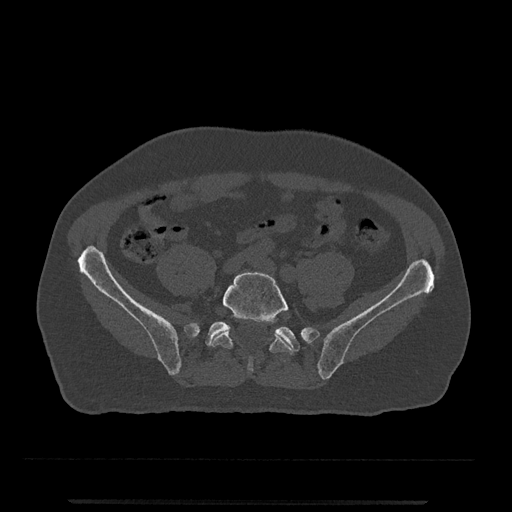
CT including the spine, one axial slice. Slice 54 of 797 in the series (ordered by position). Reconstruction kernel Br40s/3. 120 kVp. Bone window (W 1800 / L 400 HU). 0.5 mm slice thickness. 512 × 512 image matrix. Male patient, age 63 years. Case-level facts recorded for this patient, not image findings: primary cancer: prostate.
Outlined on this slice (semi-automatically segmented with operator editing):
- L5 vertebra: box from (x=210, y=272) to (x=293, y=372) px